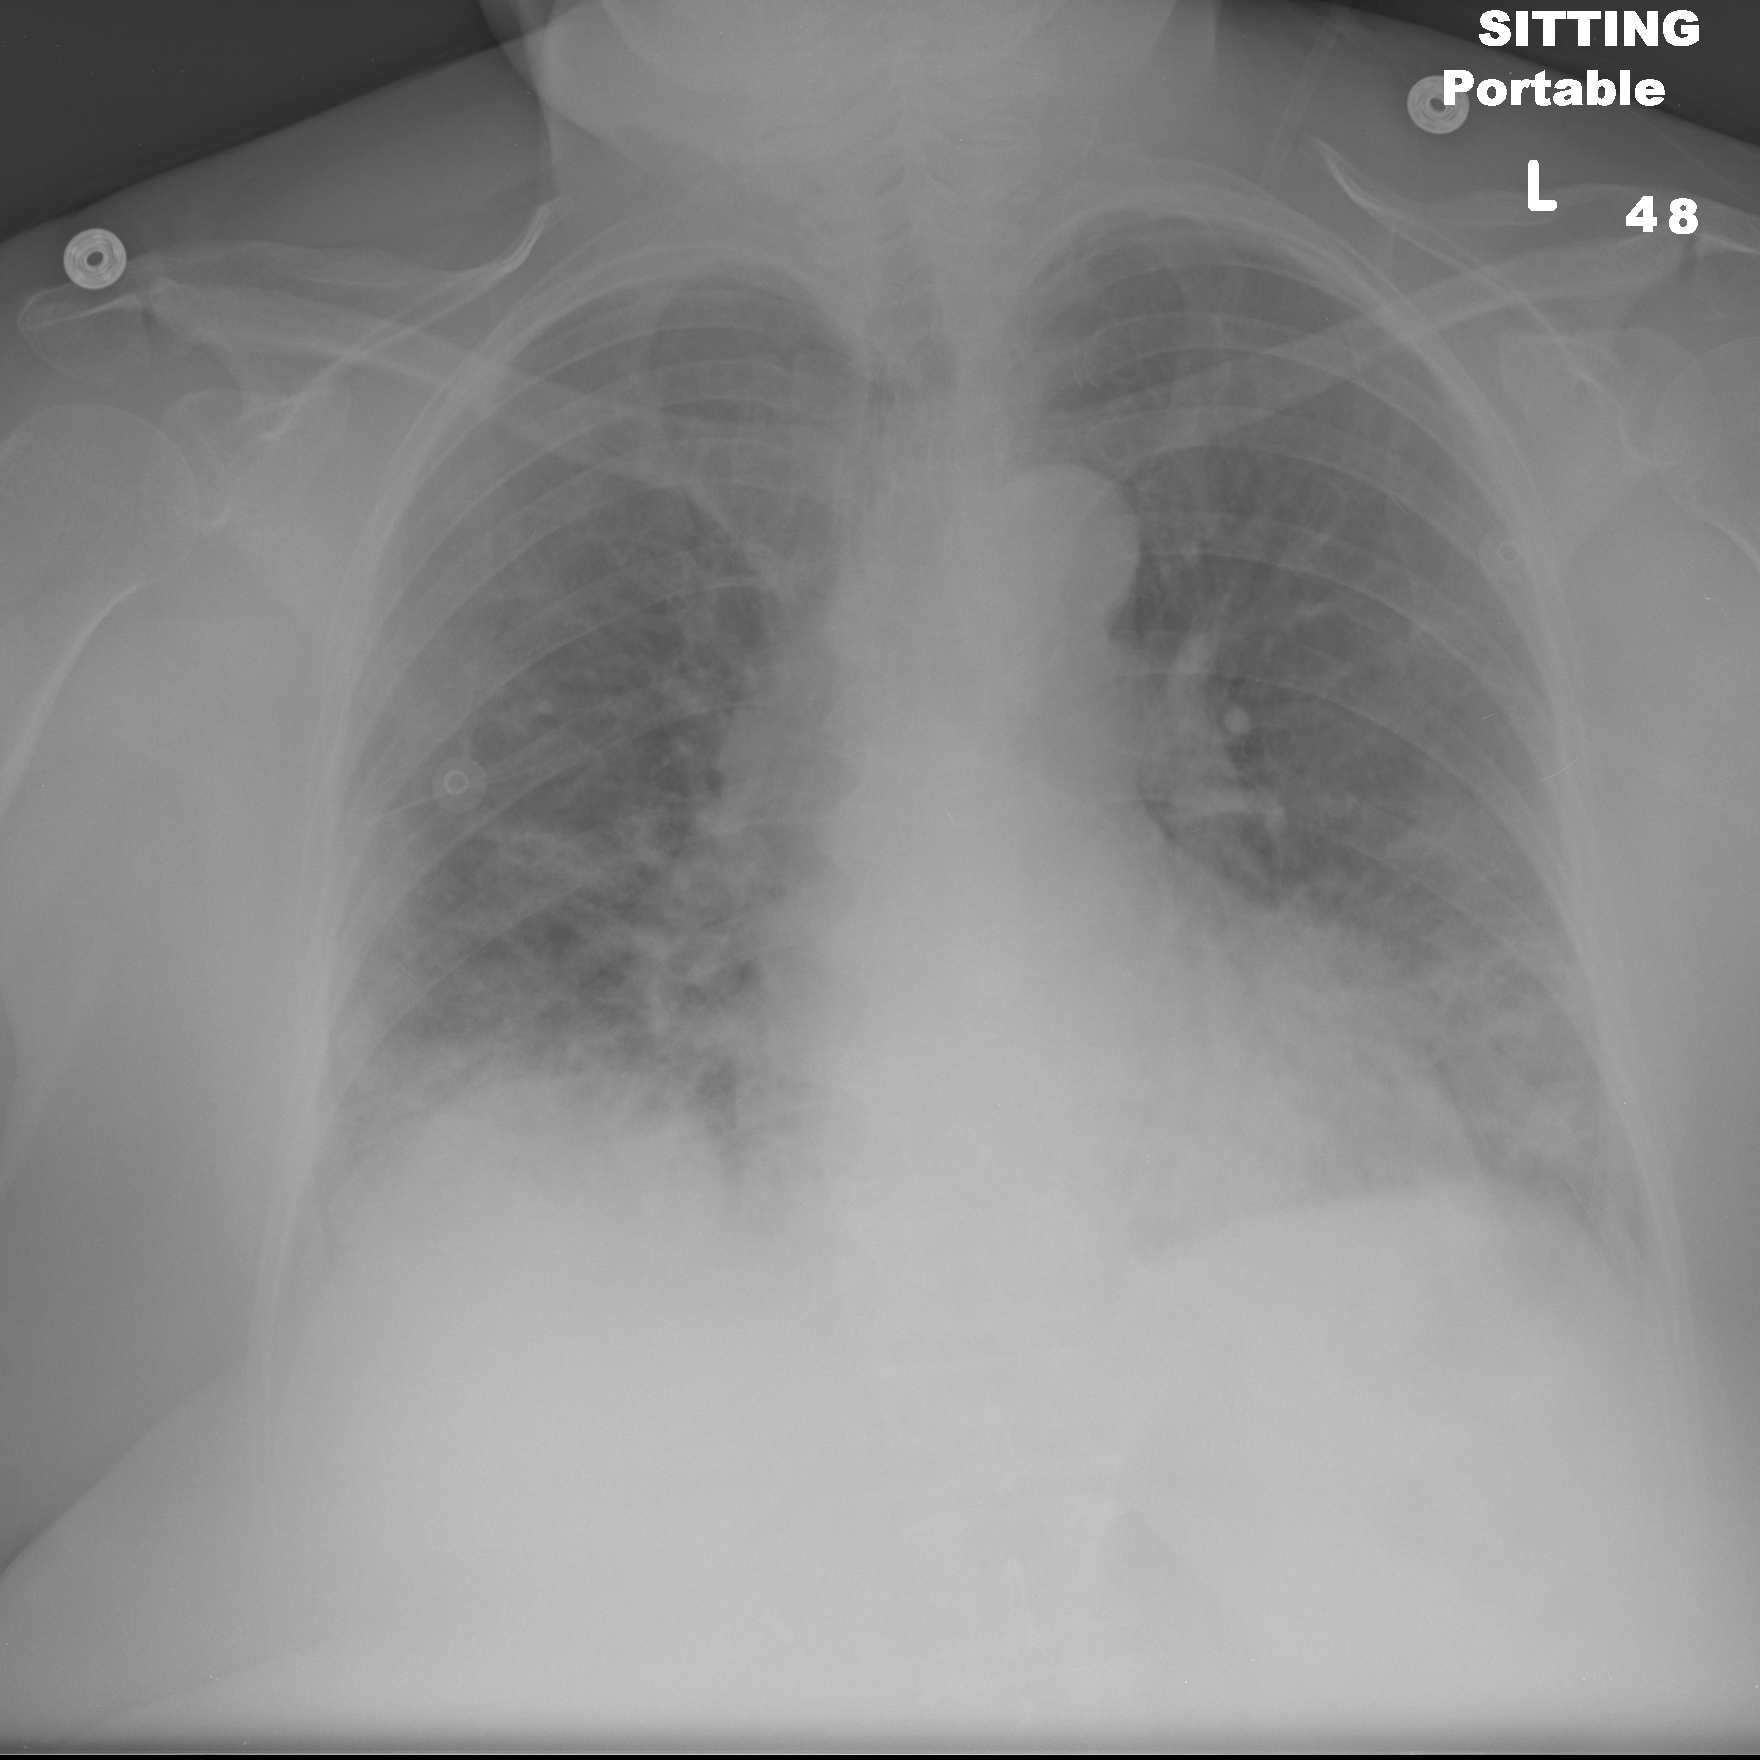
Chest X-ray (portable), AP projection. Female patient, age 67 years; imaged 2 days after the COVID-19 diagnosis.
Radiologist's key findings for this exam: Worsening bilateral airspace disease is seen within the lower lobes.